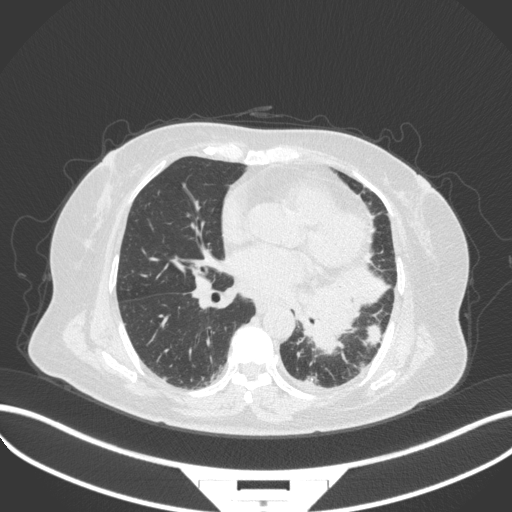
Chest CT, one axial slice; slice 163 of 328 in the series (ordered by position); reconstruction kernel B31f; lung window (W 1500 / L -600 HU); 512 × 512 image matrix, field of view 400 × 400 mm. Patient: female, 69 years. From the clinical record (not read from this slice): clinical TNM (as recorded): T2b N3 M1.
Structures marked on this image (bounding box drawn by a radiologist):
- lung tumour (recorded histology: adenocarcinoma): bounding box [x1, y1, x2, y2] px = [299, 272, 390, 357]